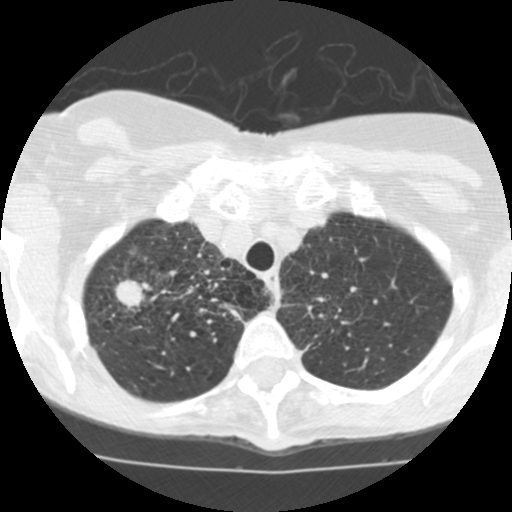
Low-dose screening chest CT, axial slice. Second screening round (one year after baseline). Lung window (W 1500 / L -600 HU). 2.5 mm slice thickness. 512 × 512 image matrix, field of view 280 × 280 mm. Female participant, aged 68 years at enrolment. Current smoker at enrolment.
Expert-annotated lung lesion, bounding box <88,266,157,337> (left, top, right, bottom; pixels). The screening reader recorded 3 non-calcified nodules or masses ≥4 mm on this exam; which of them this box marks is not recorded.